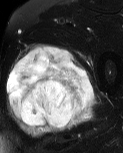
MRI of an extremity soft-tissue mass, one axial slice; position 34 of 60 along the scan axis; T2-weighted fat-saturated; MR volume resampled by the dataset authors to the PET/CT grid (not the native acquisition matrix); 3.27 mm slice thickness; 123 × 153 image matrix. Male patient. Case-level facts recorded for this patient, not image findings: histological type: pleiomorphic liposarcoma; grade: high; site of the primary tumour: left thigh.
Structures marked on this image (expert contour drawn on MRI and transferred to this co-registered scan by the dataset authors):
- gross tumour volume including surrounding oedema: bounding box [x1, y1, x2, y2] px = [6, 43, 96, 137]
- gross tumour volume (mass): [6, 45, 94, 128]